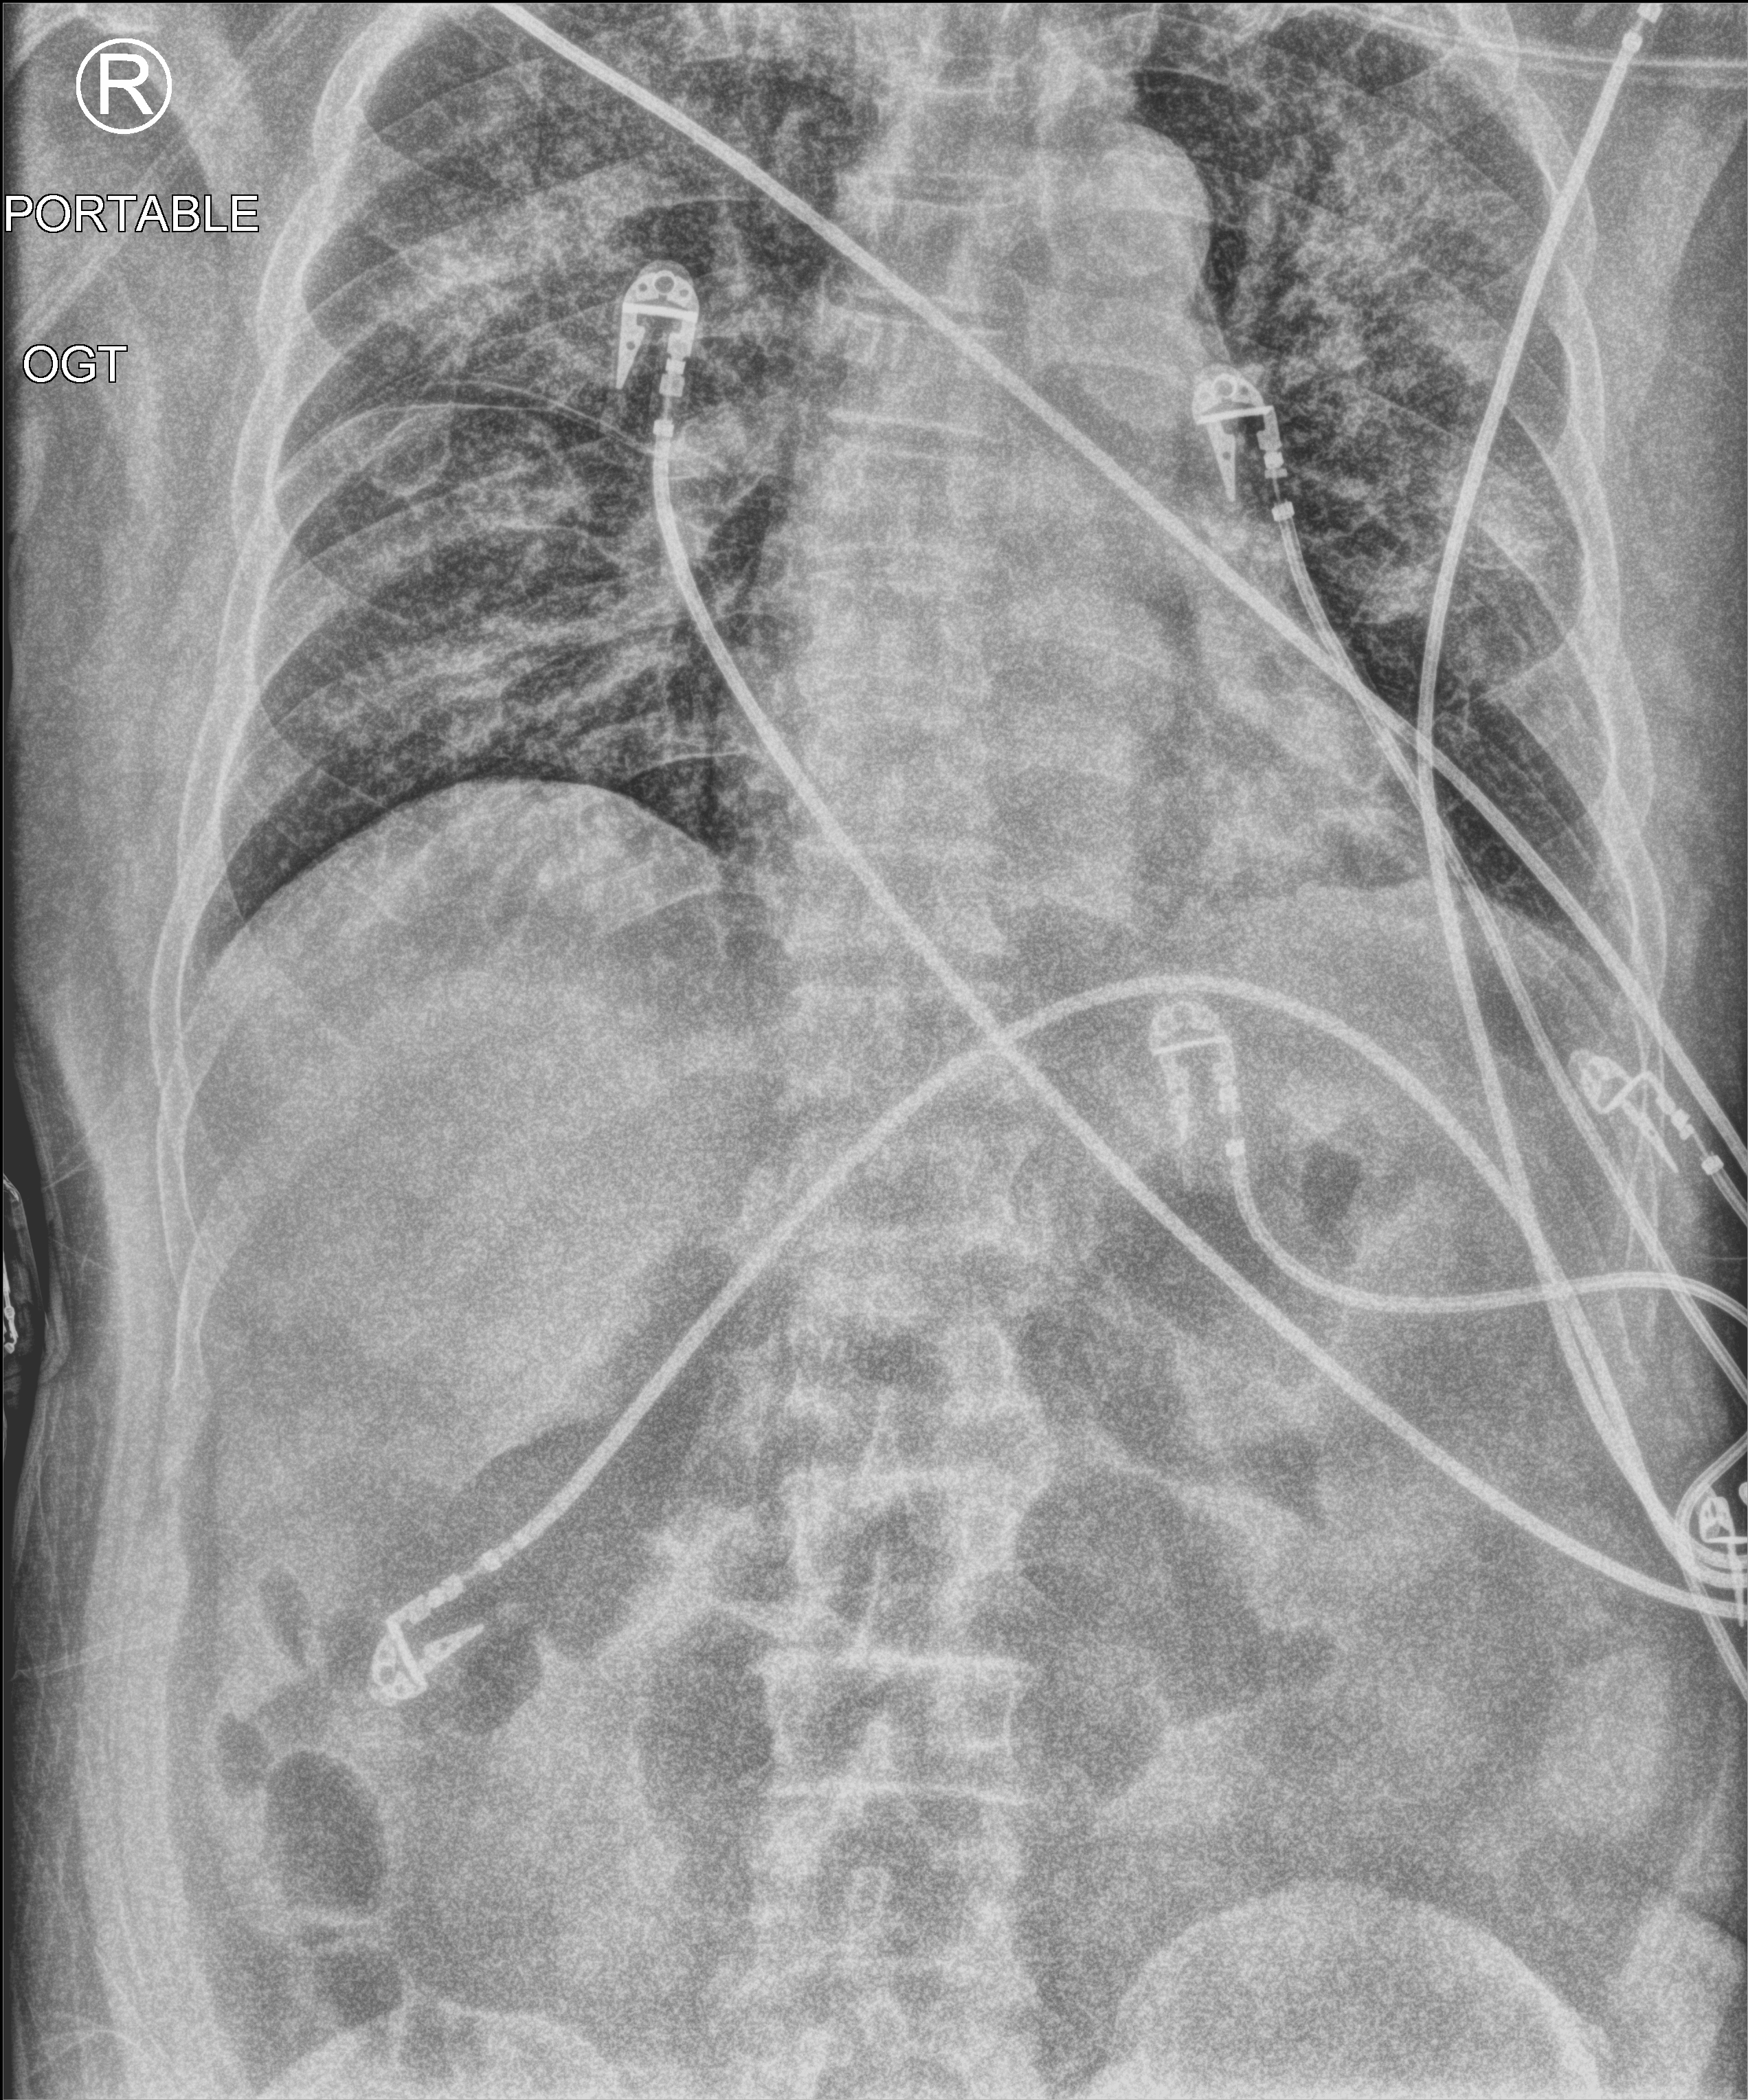
Chest X-ray (portable); anteroposterior (AP) projection. Male patient hospitalised with COVID-19, age 60–74 years.
Admission-level facts for this patient (not findings on this image; timing relative to this image not recorded): admitted to intensive care during this hospital stay: yes.